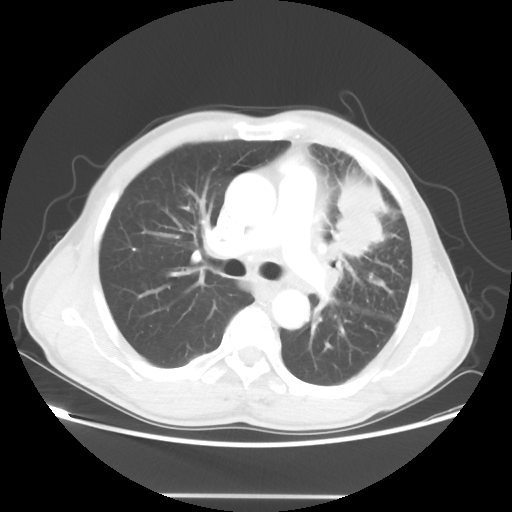
Chest CT, one axial slice. Position 32 of 55 along the scan axis. Reconstruction kernel STANDARD. Lung window (W 1500 / L -600 HU). 5 mm slice thickness. 512 × 512 image matrix. Male patient, age 60 years. Case-level facts recorded for this patient, not image findings: clinical TNM (as recorded): T3 N3 M0.
Structures marked on this image (rectangle marked by the reading radiologist):
- lung tumour (recorded histology: adenocarcinoma): bounding box [x1, y1, x2, y2] px = [333, 176, 387, 258]